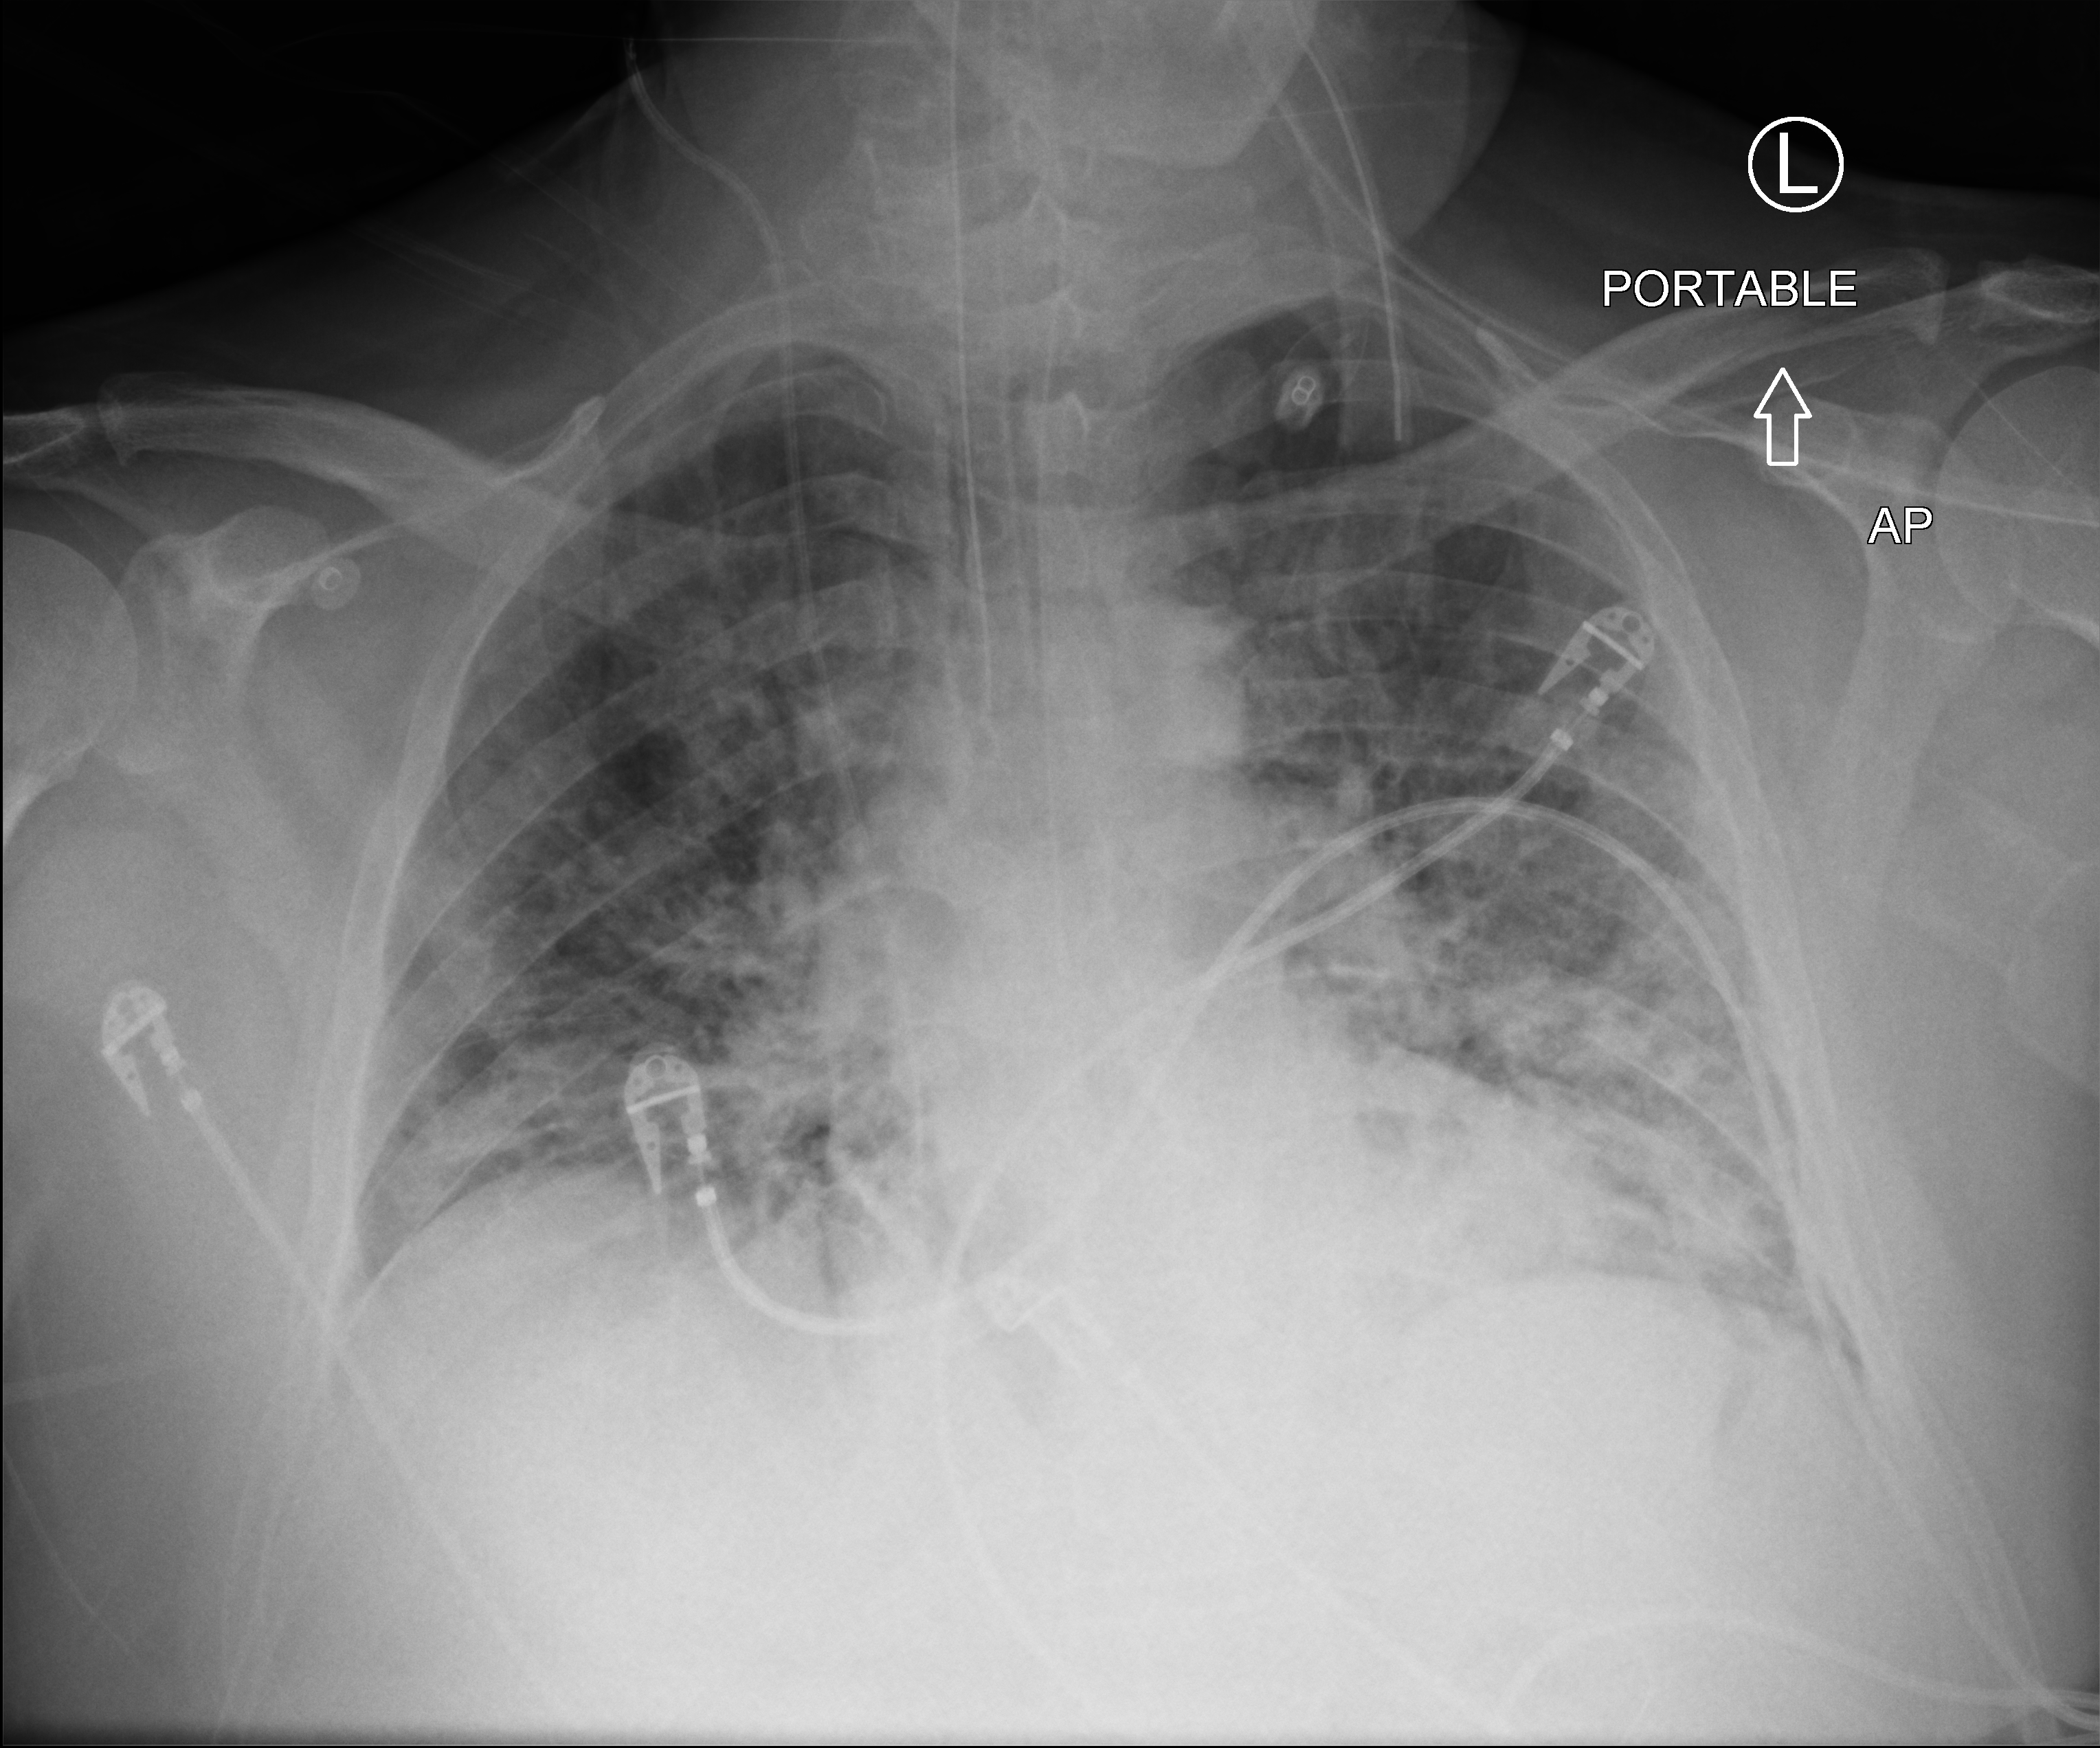
Portable chest radiograph, anteroposterior (AP) projection. Male patient hospitalised with COVID-19, age 18–59 years.
From the hospital-stay record, not from the radiograph (when in the stay this image was taken is not recorded):
- admitted to intensive care during this hospital stay: yes